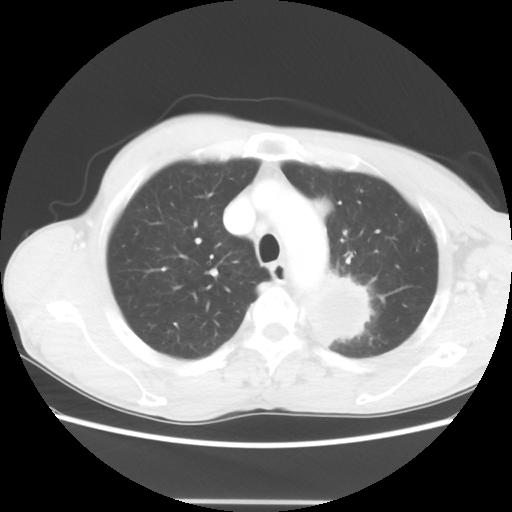
Chest CT, one axial slice; reconstruction kernel STANDARD; 100 kVp; lung window (W 1500 / L -600 HU); 512 × 512 image matrix, field of view 360 × 360 mm. Male patient, age 61 years. Case-level facts recorded for this patient, not image findings: clinical TNM (as recorded): T3 N1 M1.
Structures marked on this image (bounding box drawn by a radiologist):
- lung tumour (recorded histology: adenocarcinoma): bounding box <304,264,372,349> (left, top, right, bottom; pixels)
- lung tumour (recorded histology: adenocarcinoma): <313,194,327,218>